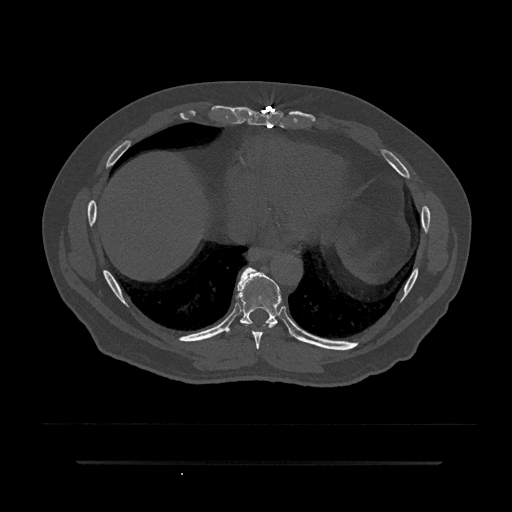
CT including the spine, one axial slice; slice 400 of 797 in the series (ordered by position); reconstruction kernel Br40s/3; 120 kVp; bone window (W 1800 / L 400 HU); 0.5 mm slice thickness; 512 × 512 image matrix, field of view 464 × 464 mm. Patient: male, 59 years. Case-level facts recorded for this patient, not image findings: primary cancer: bile ducts; vertebrae with lytic lesions (as recorded): T10.
Outlined on this slice (semi-automatic segmentation, software-assisted and operator-edited):
- T8 vertebra: bounding box [x1, y1, x2, y2] px = [251, 324, 274, 350]
- T9 vertebra: [227, 267, 282, 333]